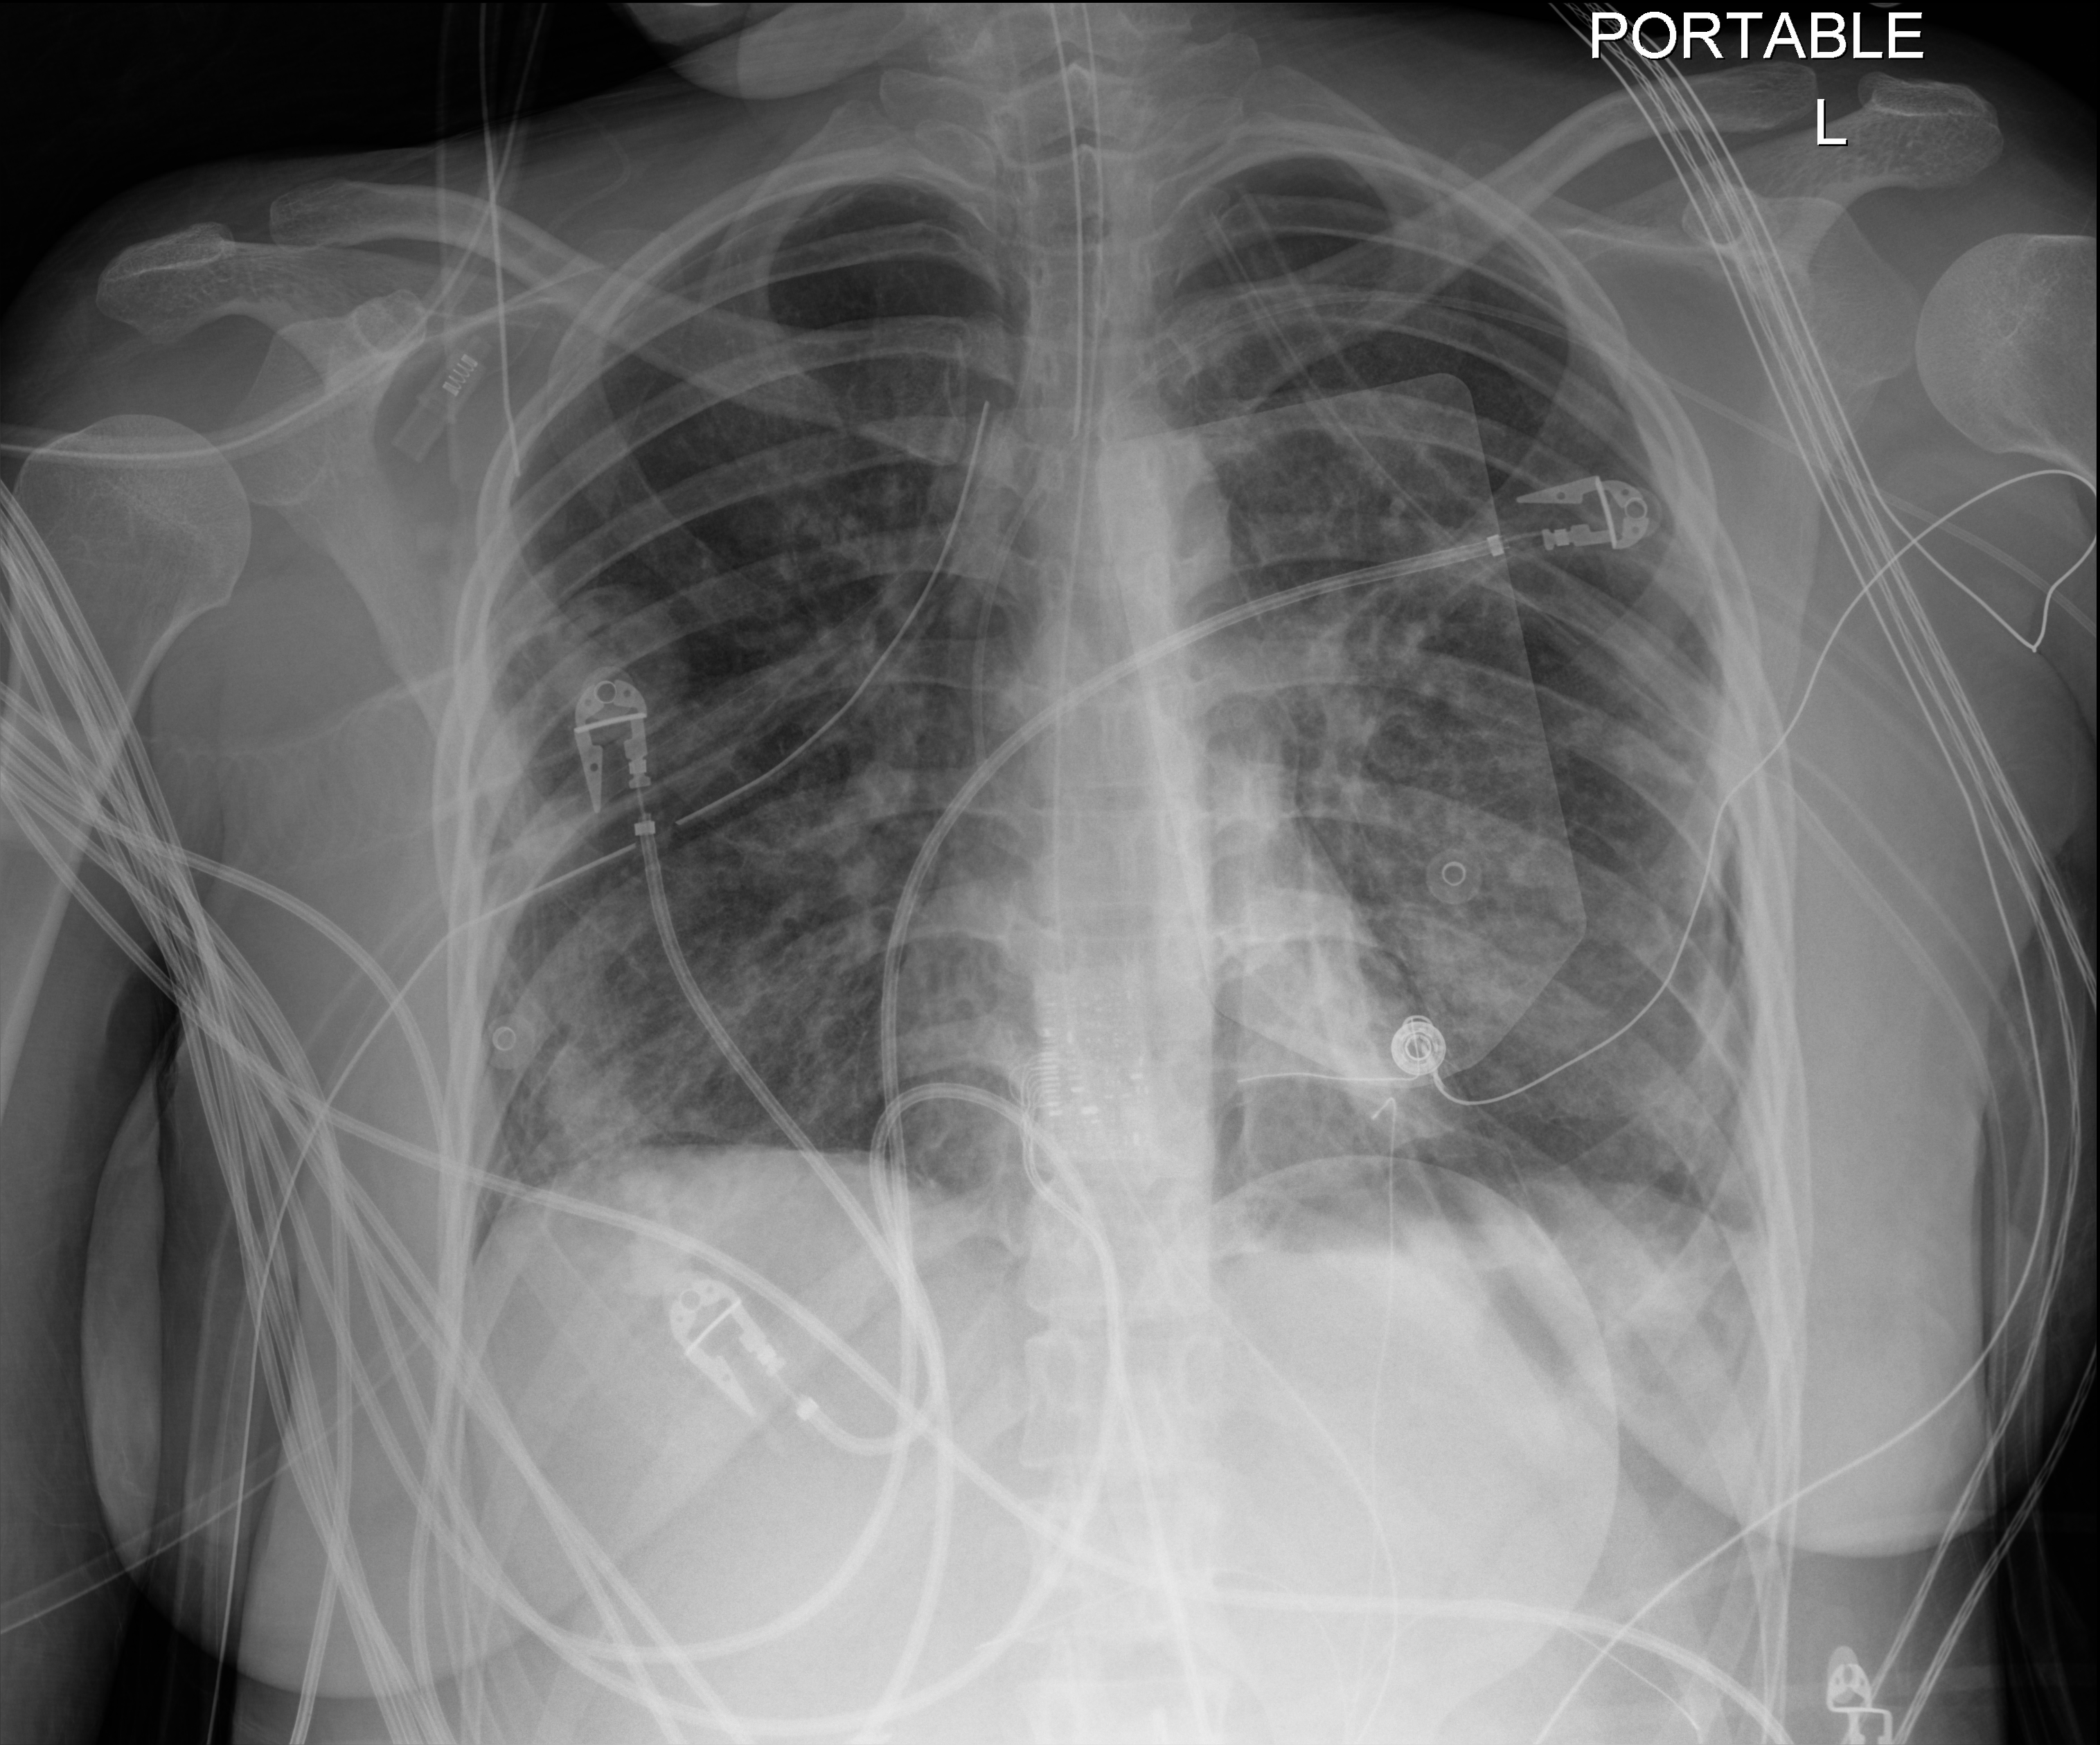
Portable chest radiograph; anteroposterior (AP) projection. Adult patient hospitalised with COVID-19, age 18–59 years.
Admission-level facts for this patient (not findings on this image; timing relative to this image not recorded): diabetes (admission record): no; admitted to intensive care during this hospital stay: yes.